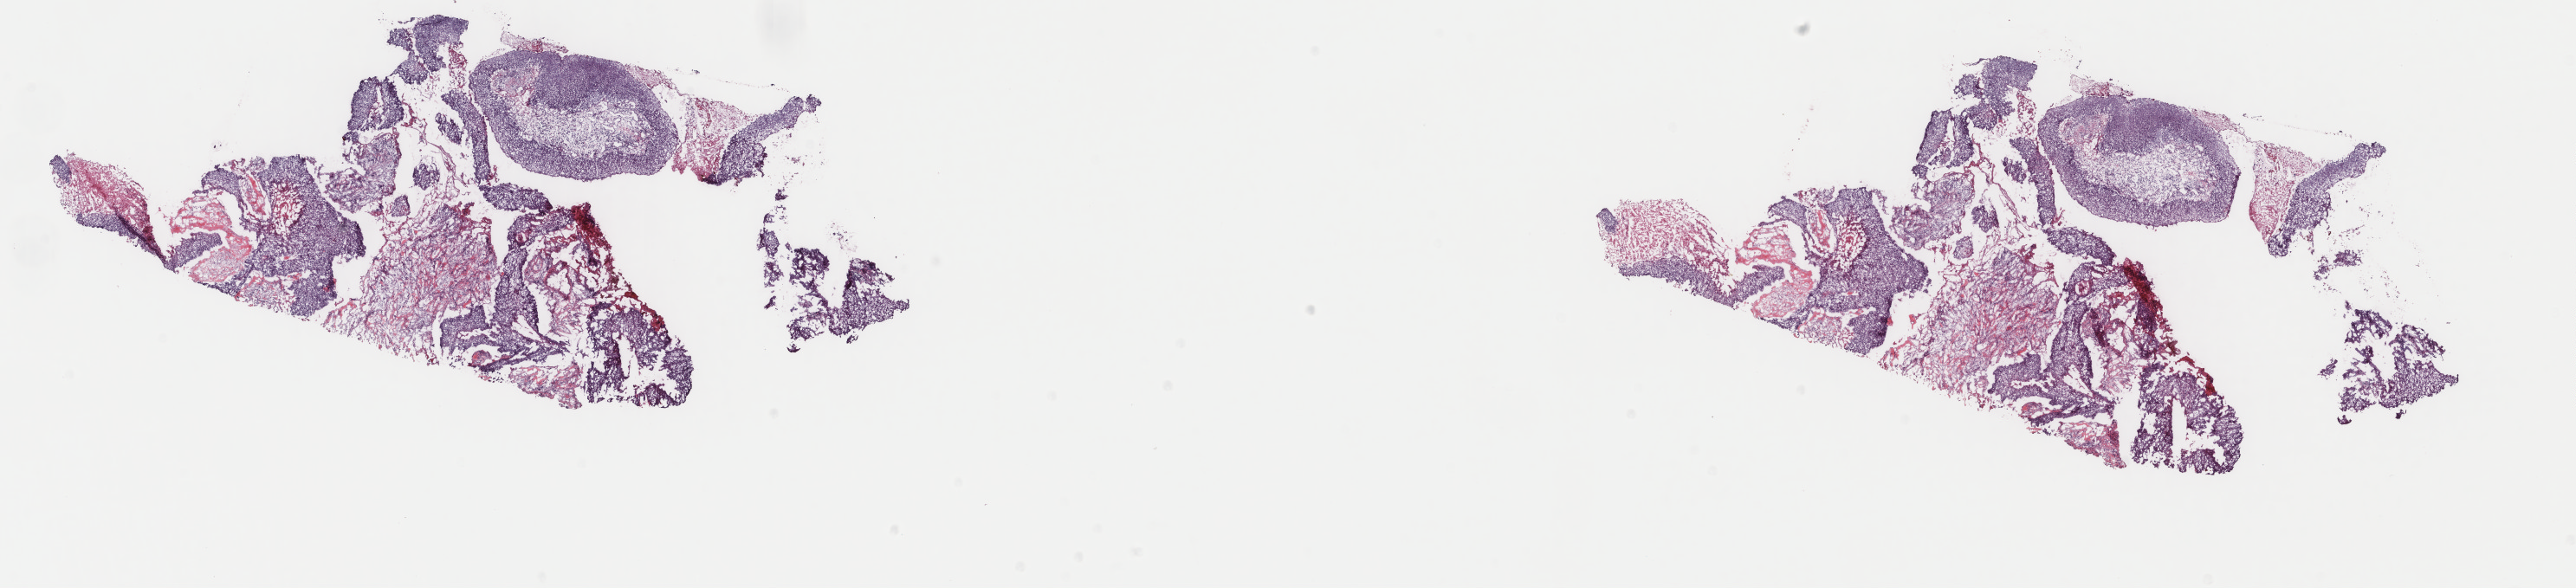
Digitized H&E-stained tissue section (whole slide), whole scanned area (about 23.6 x 5.4 mm, slide scanned at 40x) shown as a low-resolution overview; frozen section from the top of the tissue portion; cervix, primary tumour sample. Female, age 44 years at initial diagnosis. Histologic grade: GX (grade cannot be assessed). Pathologist review of this section (percent, as recorded): tumour cells 60%, tumour nuclei 60%, normal cells 0%, stromal cells 35%, necrosis 5%. Inflammatory infiltration, as recorded: lymphocyte infiltration 5%, monocyte infiltration 5%, neutrophil infiltration 5%.
• FIGO stage: I
• histologic diagnosis: Squamous cell carcinoma, large cell, nonkeratinizing, NOS (cervix uteri)